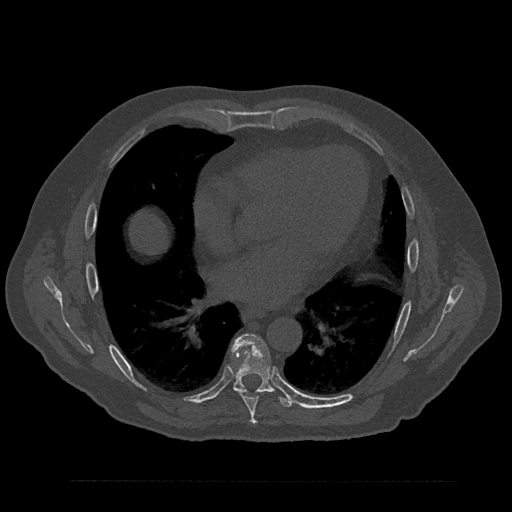
CT including the spine, one axial slice; position 480 of 797 along the scan axis; reconstruction kernel Br40s/3; 120 kVp; bone window (W 1800 / L 400 HU); 0.5 mm slice thickness; 512 × 512 image matrix, field of view 430 × 430 mm. Patient: male, 61 years. Case-level facts recorded for this patient, not image findings: primary cancer: prostate.
Structures marked on this image (semi-automatic segmentation, software-assisted and operator-edited):
- T7 vertebra: bounding box (x1, y1, x2, y2) in pixels: (238, 391, 260, 425)
- T8 vertebra: (231, 335, 294, 407)